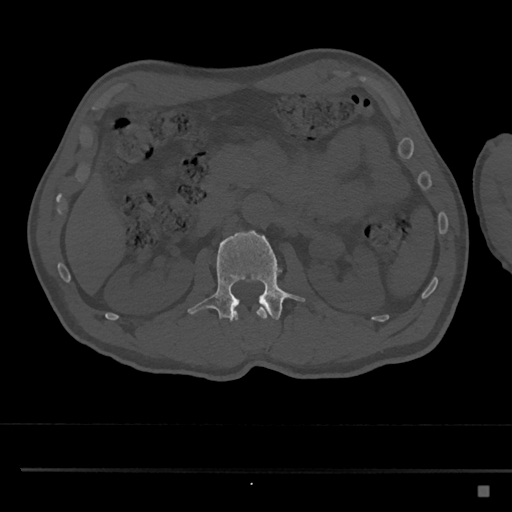
CT including the spine, one axial slice; position 775 of 797 along the scan axis; reconstruction kernel Br40s/3; 120 kVp; bone window (W 1800 / L 400 HU); 512 × 512 image matrix, field of view 391 × 391 mm. Patient: male, 59 years. Case-level facts recorded for this patient, not image findings: primary cancer: prostate.
Structures marked on this image (semi-automatically segmented with operator editing):
- L1 vertebra: box from (x=231, y=307) to (x=268, y=320) px
- L2 vertebra: (x=188, y=230)–(x=306, y=321)